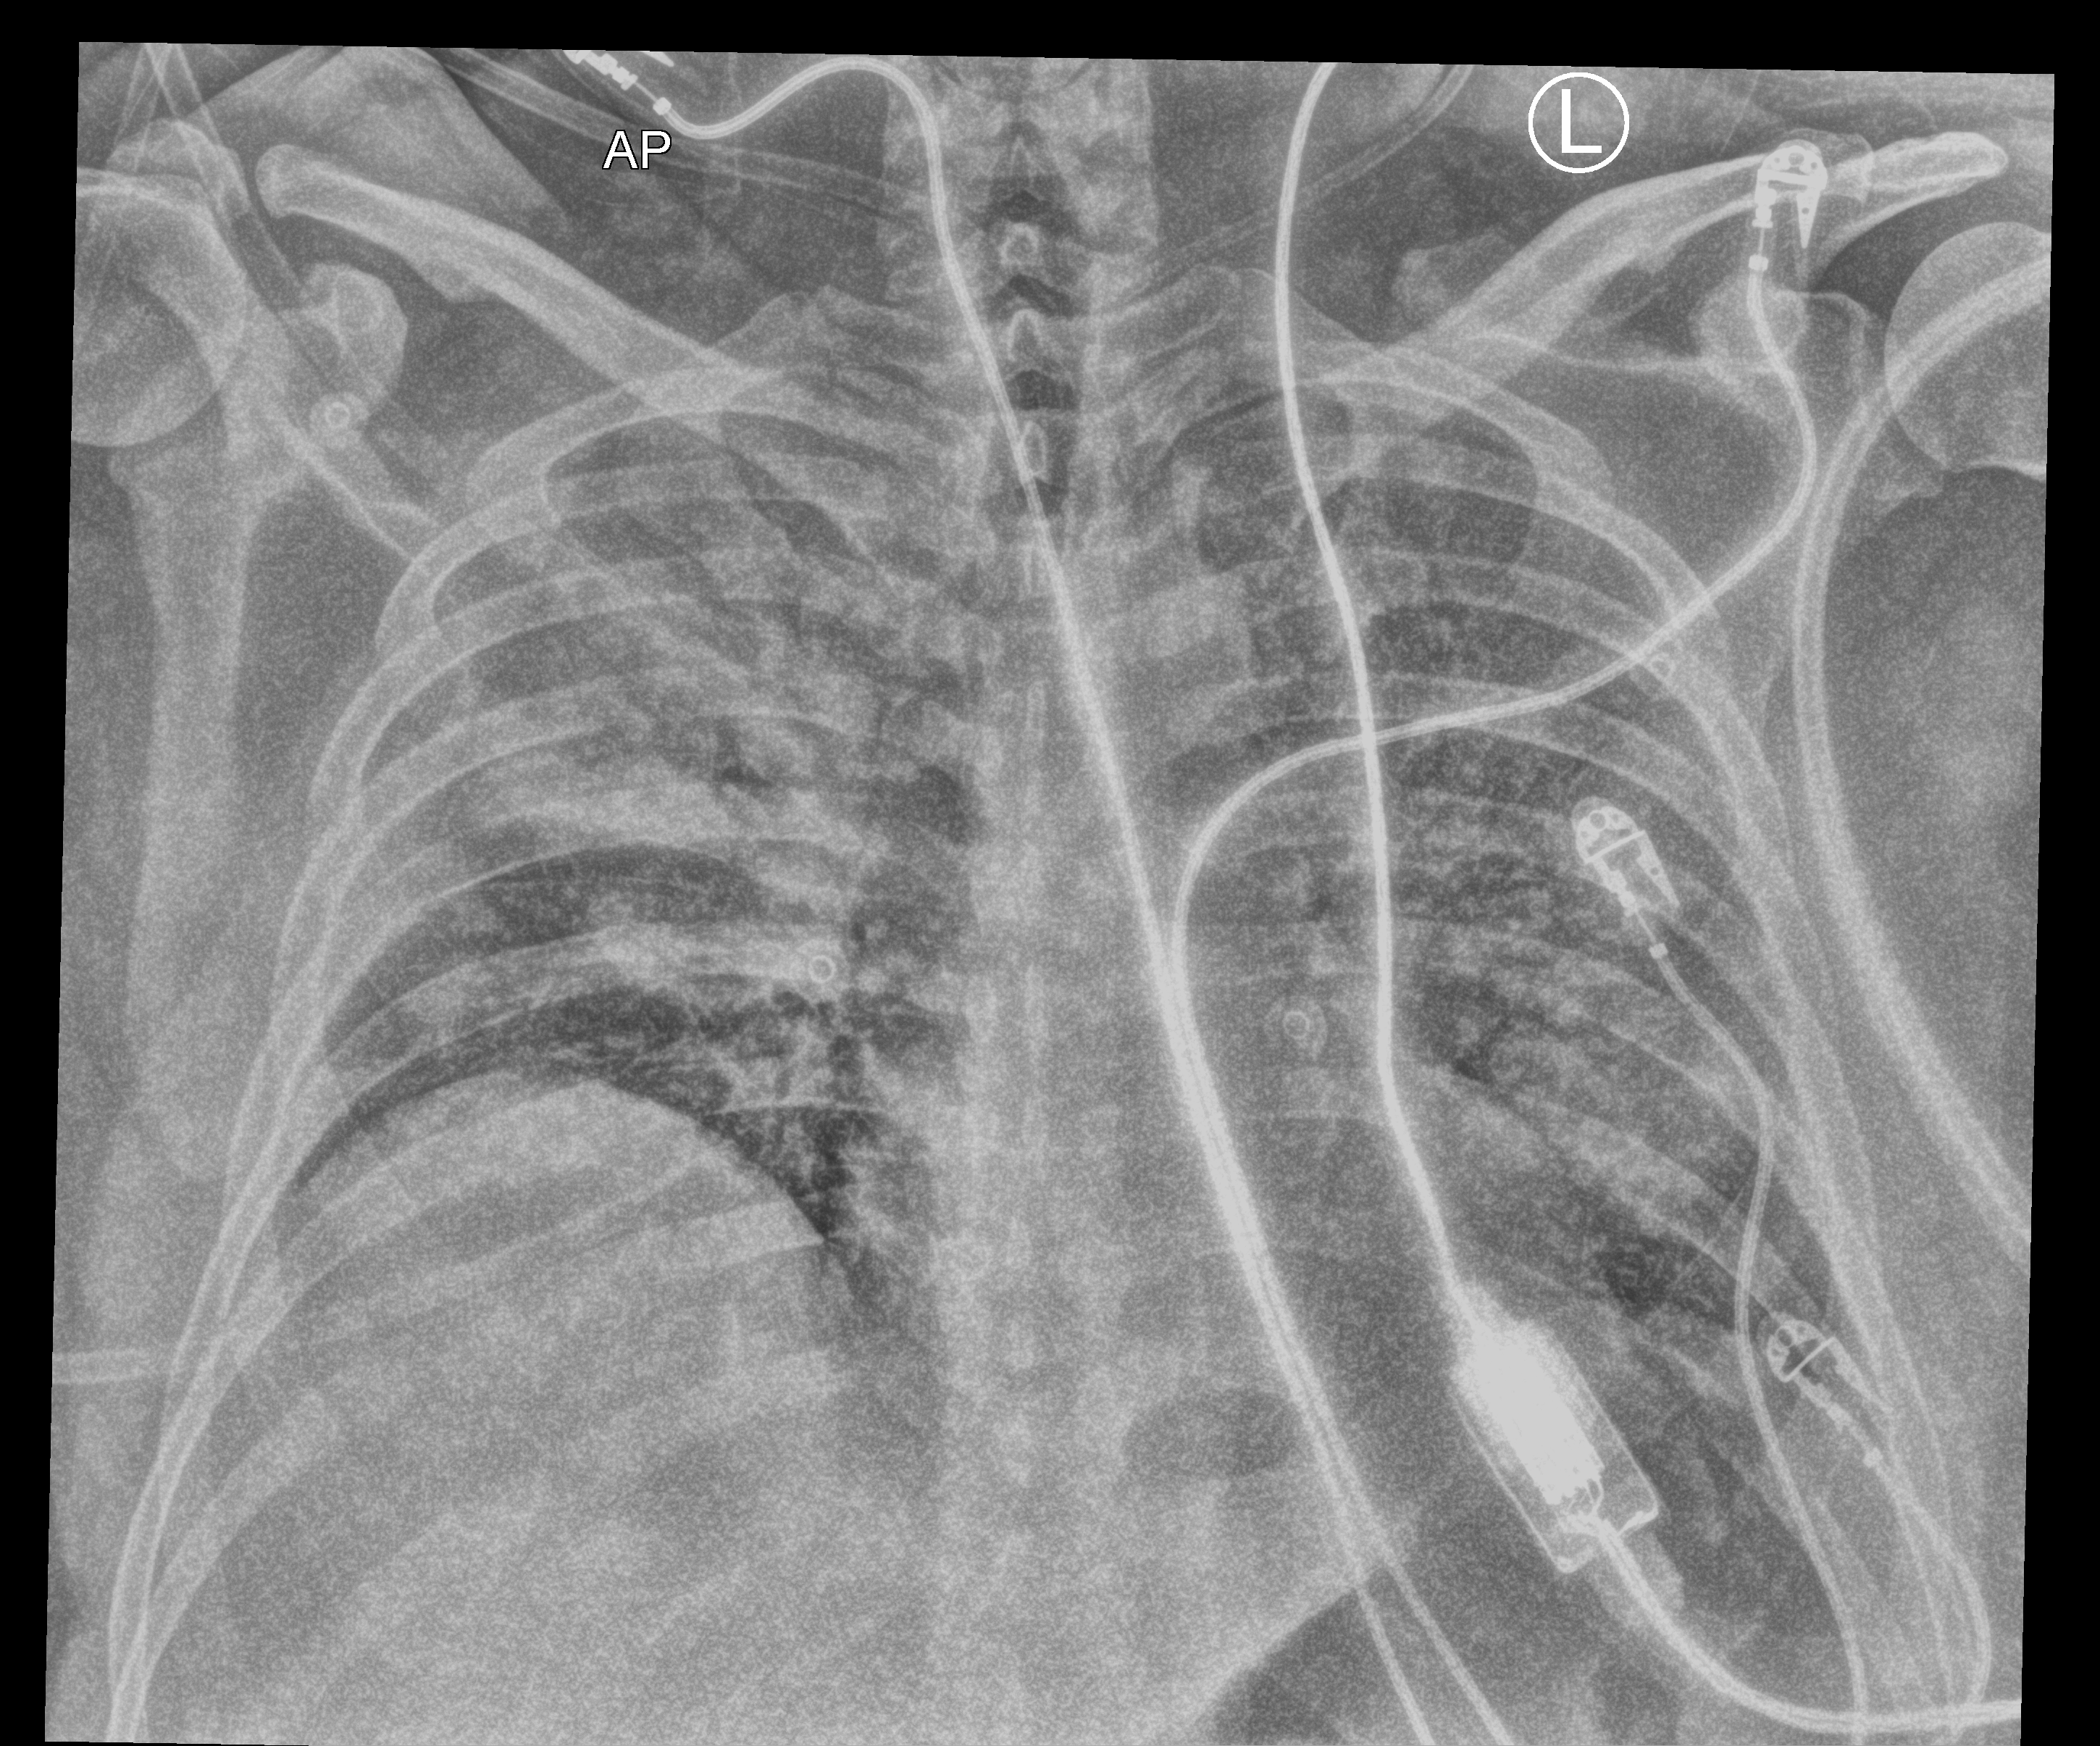
Chest X-ray (portable), anteroposterior (AP) projection. Patient hospitalised with COVID-19; male, aged 18–59 years.
Admission-level facts for this patient (not findings on this image; timing relative to this image not recorded):
- COPD (admission record): no
- mechanically ventilated during this hospital stay: yes
- admitted to intensive care during this hospital stay: yes